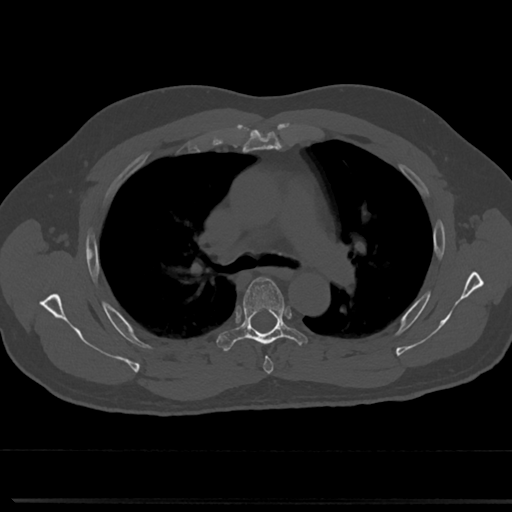
CT including the spine, one axial slice; slice 507 of 817 in the series (ordered by position); reconstruction kernel Br40s/3; 120 kVp; bone window (W 1800 / L 400 HU); 512 × 512 image matrix, field of view 355 × 355 mm. Male patient, age 61 years. Case-level facts recorded for this patient, not image findings: primary cancer: prostate.
Outlined on this slice (semi-automatic segmentation, software-assisted and operator-edited):
- T4 vertebra: bounding box [x1, y1, x2, y2] px = [261, 344, 273, 374]
- T5 vertebra: [218, 276, 310, 352]